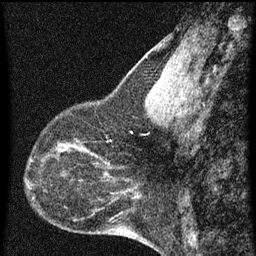
Breast MRI (dynamic contrast-enhanced), one sagittal slice; dynamic contrast-enhanced series, image 2 of 3 at this slice position (ordered by acquisition); 1.5 T; TE 4.2 ms, TR 8 ms; 2 mm slice thickness; 256 × 256 image matrix, field of view 180 × 180 mm. Female patient, age 44 years.
Annotated regions visible in this slice (semi-automatically segmented with operator editing):
- analysis volume of interest (the breast-tissue region the enhancement analysis was run in; not a lesion): bounding box <49,128,95,169> (left, top, right, bottom; pixels)
- tumour enhancement mask (voxels above the 70 % enhancement threshold inside the analysis volume of interest): <56,140,93,155>